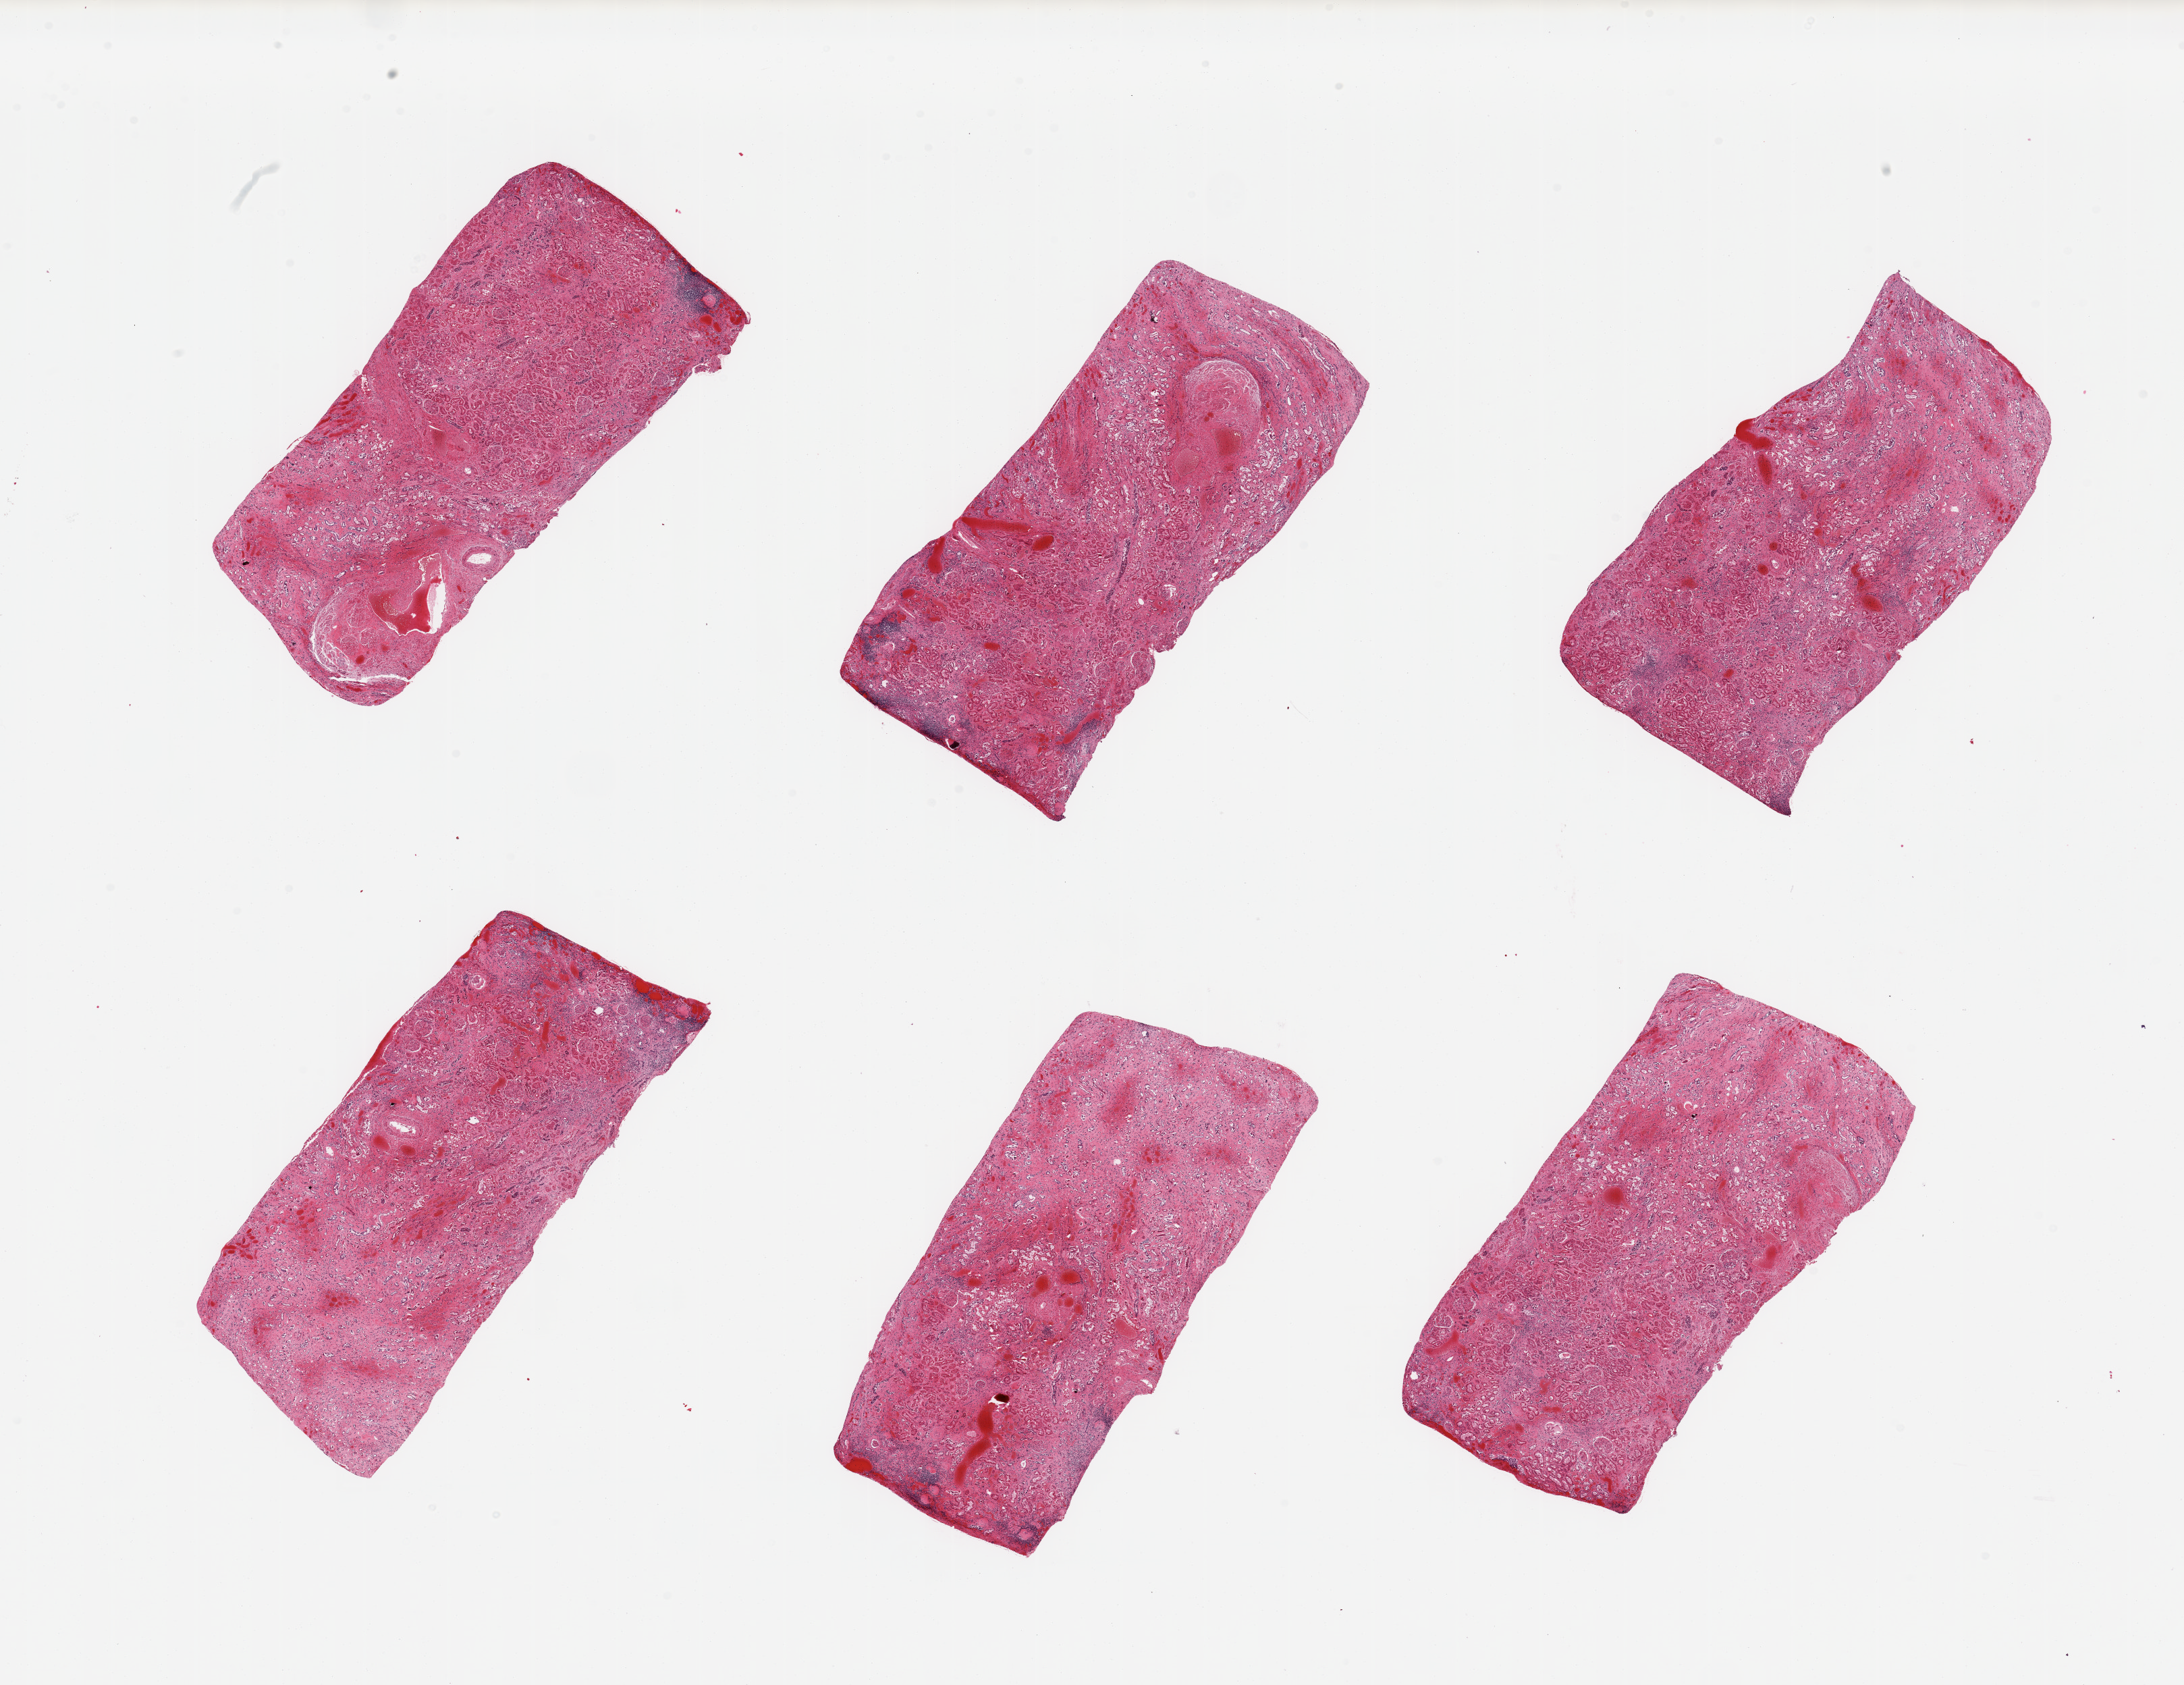
Digitized haematoxylin and eosin-stained section, brightfield, a low-resolution overview of the entire scanned area, about 25.6 x 19.7 mm. PAXgene-fixed, paraffin-embedded tissue. Section of renal cortex (target tissue). Tissue donor sample. Male donor.
* review note (as recorded): 6 pieces; moderate to severe autolysis of tubules with largely sloughed epithelium; marked congestion; arteriolo-nephrosclerosis with hyalinized glomeruli; interstitial nephritis